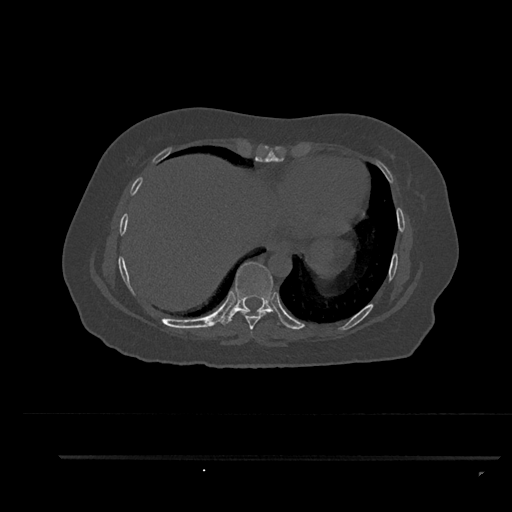
CT including the spine, one axial slice. Reconstruction kernel Br40s/3. Bone window (W 1800 / L 400 HU). 0.5 mm slice thickness. 512 × 512 image matrix, field of view 408 × 408 mm. Patient: female, 44 years. Case-level facts recorded for this patient, not image findings: primary cancer: renal; vertebrae with lytic lesions (as recorded): L1.
Annotated regions visible in this slice (semi-automatically segmented with operator editing):
- T7 vertebra: bounding box <250,331,253,335> (left, top, right, bottom; pixels)
- T8 vertebra: <237,309,268,330>
- T9 vertebra: <222,262,283,325>